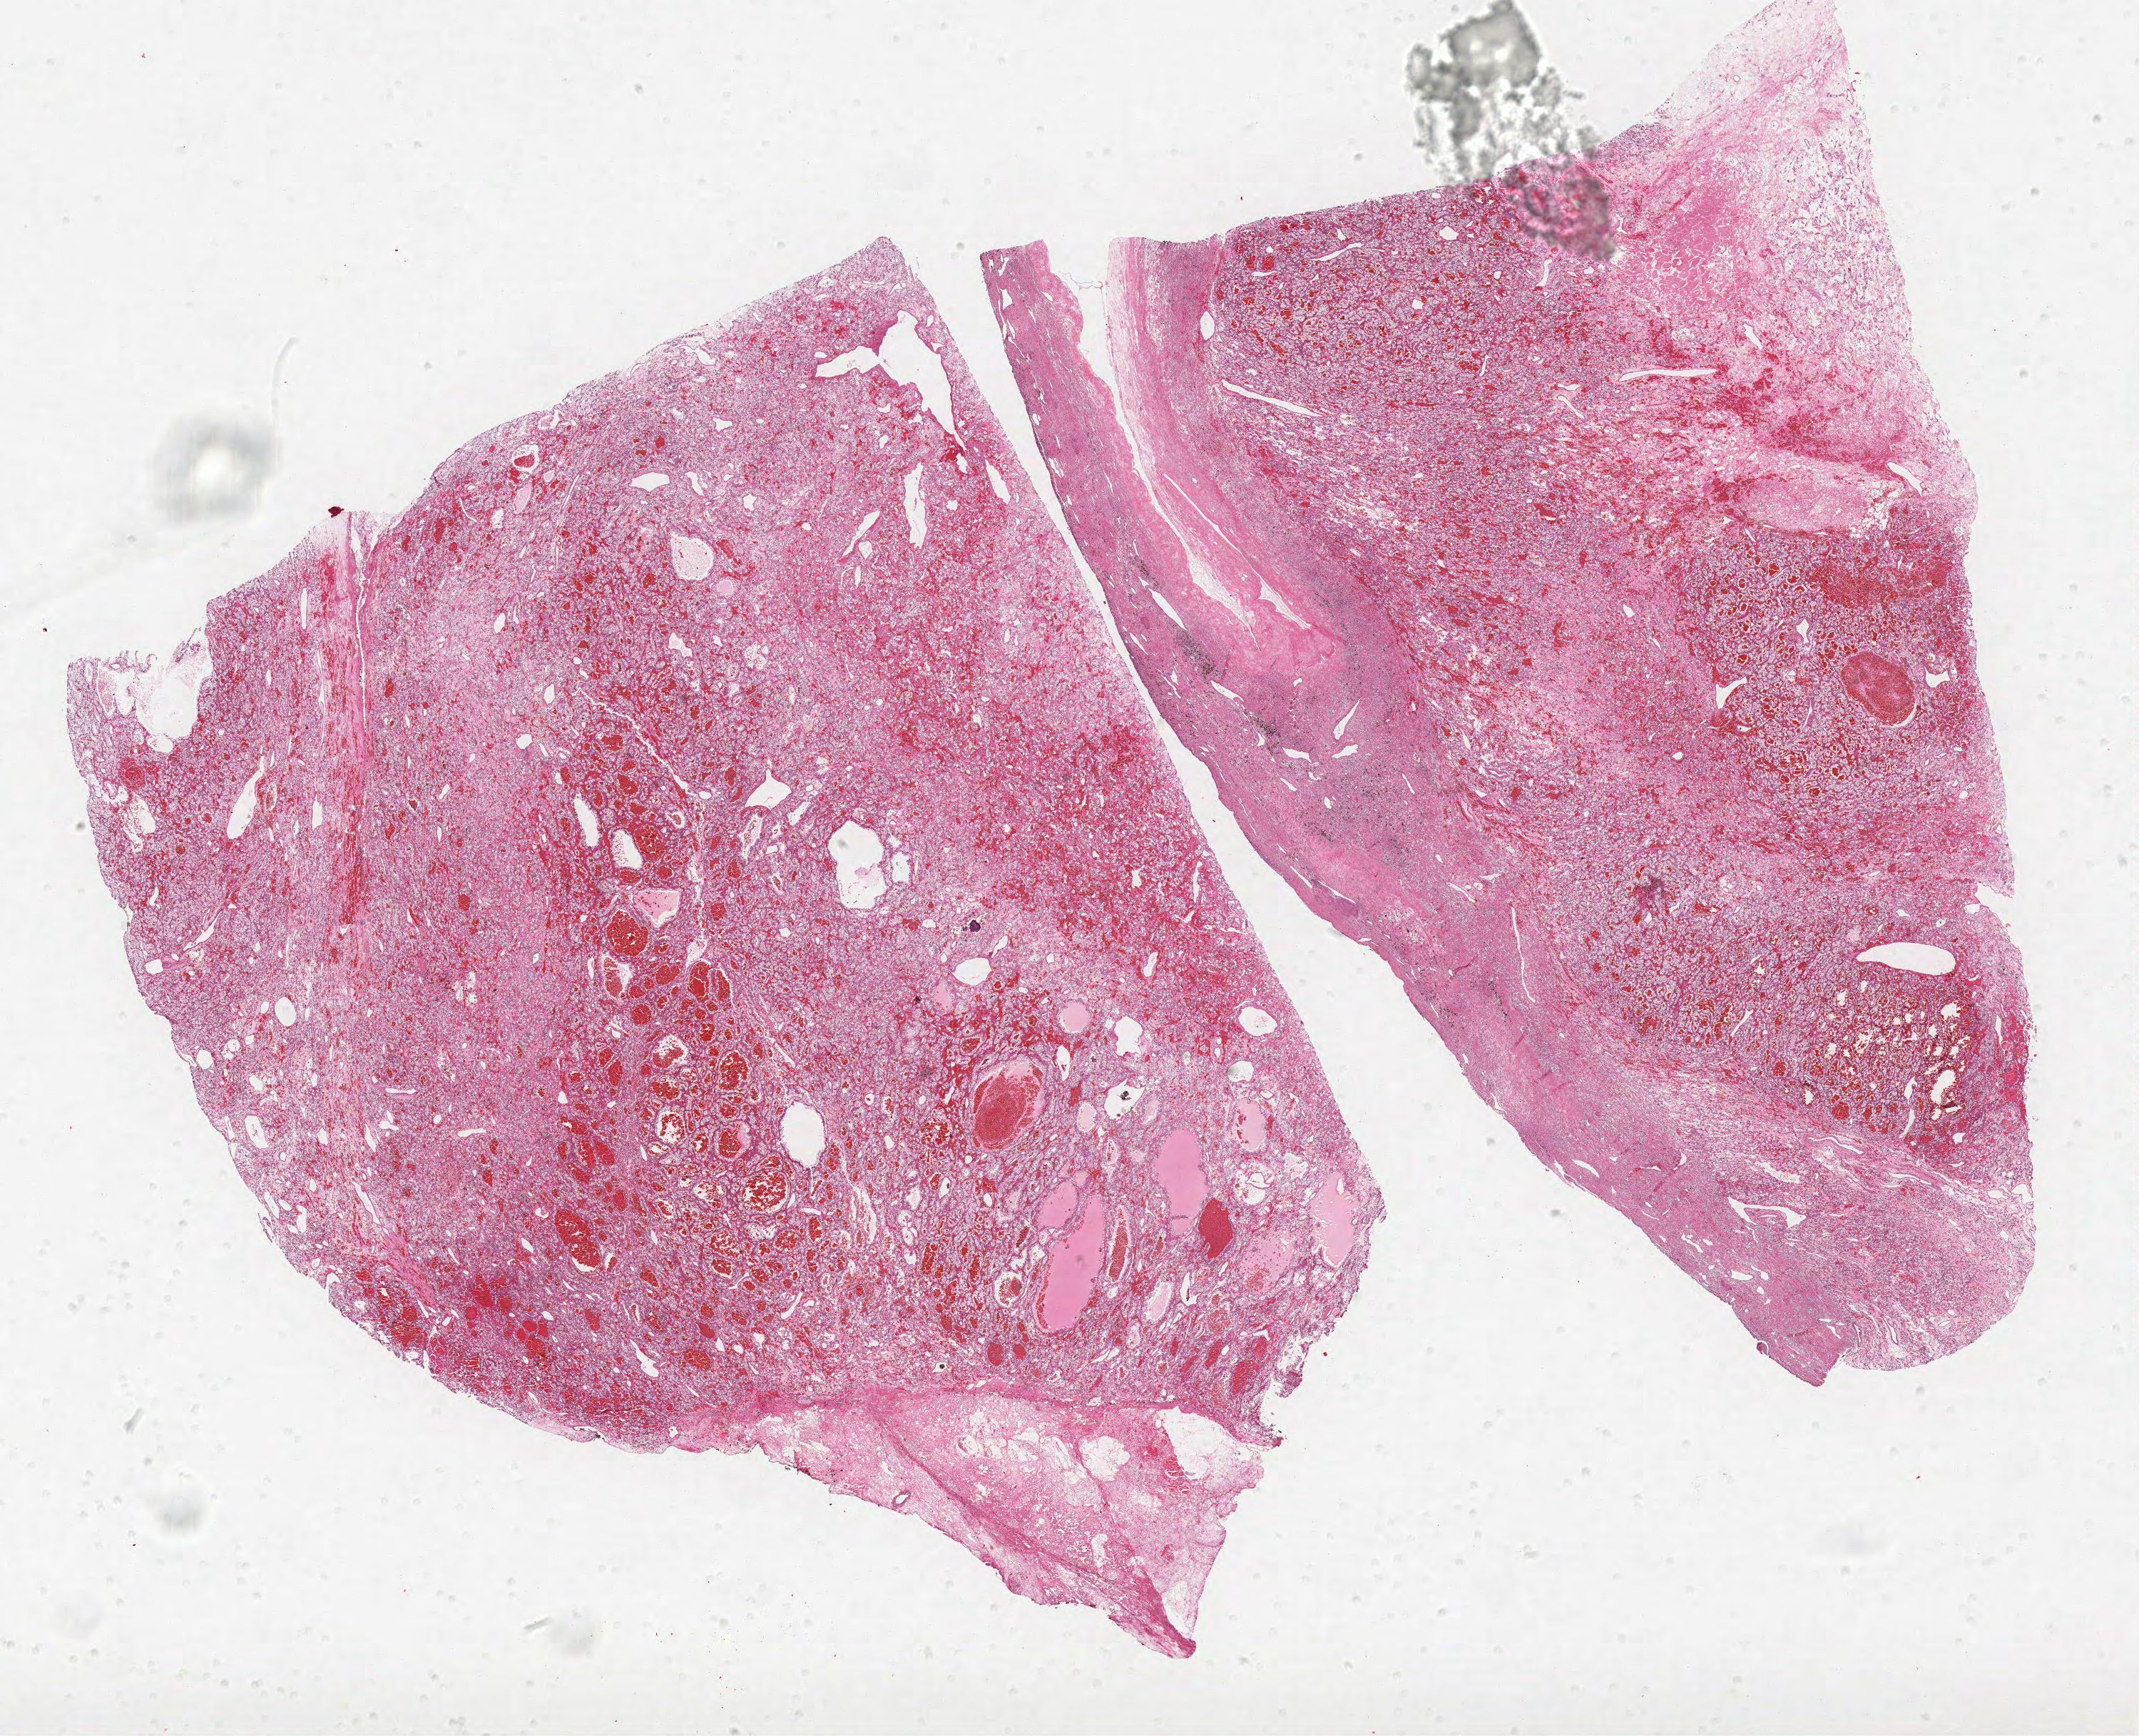
H&E-stained whole-slide image — whole scanned area (about 24.0 x 19.5 mm, slide scanned at 40x) shown as a low-resolution overview, FFPE section, sample: primary tumour, kidney. Male patient; age at initial diagnosis 61 years. Histologic grade: G2 (moderately differentiated).
• AJCC pathologic stage: I
• pathologic diagnosis: Clear cell adenocarcinoma, NOS